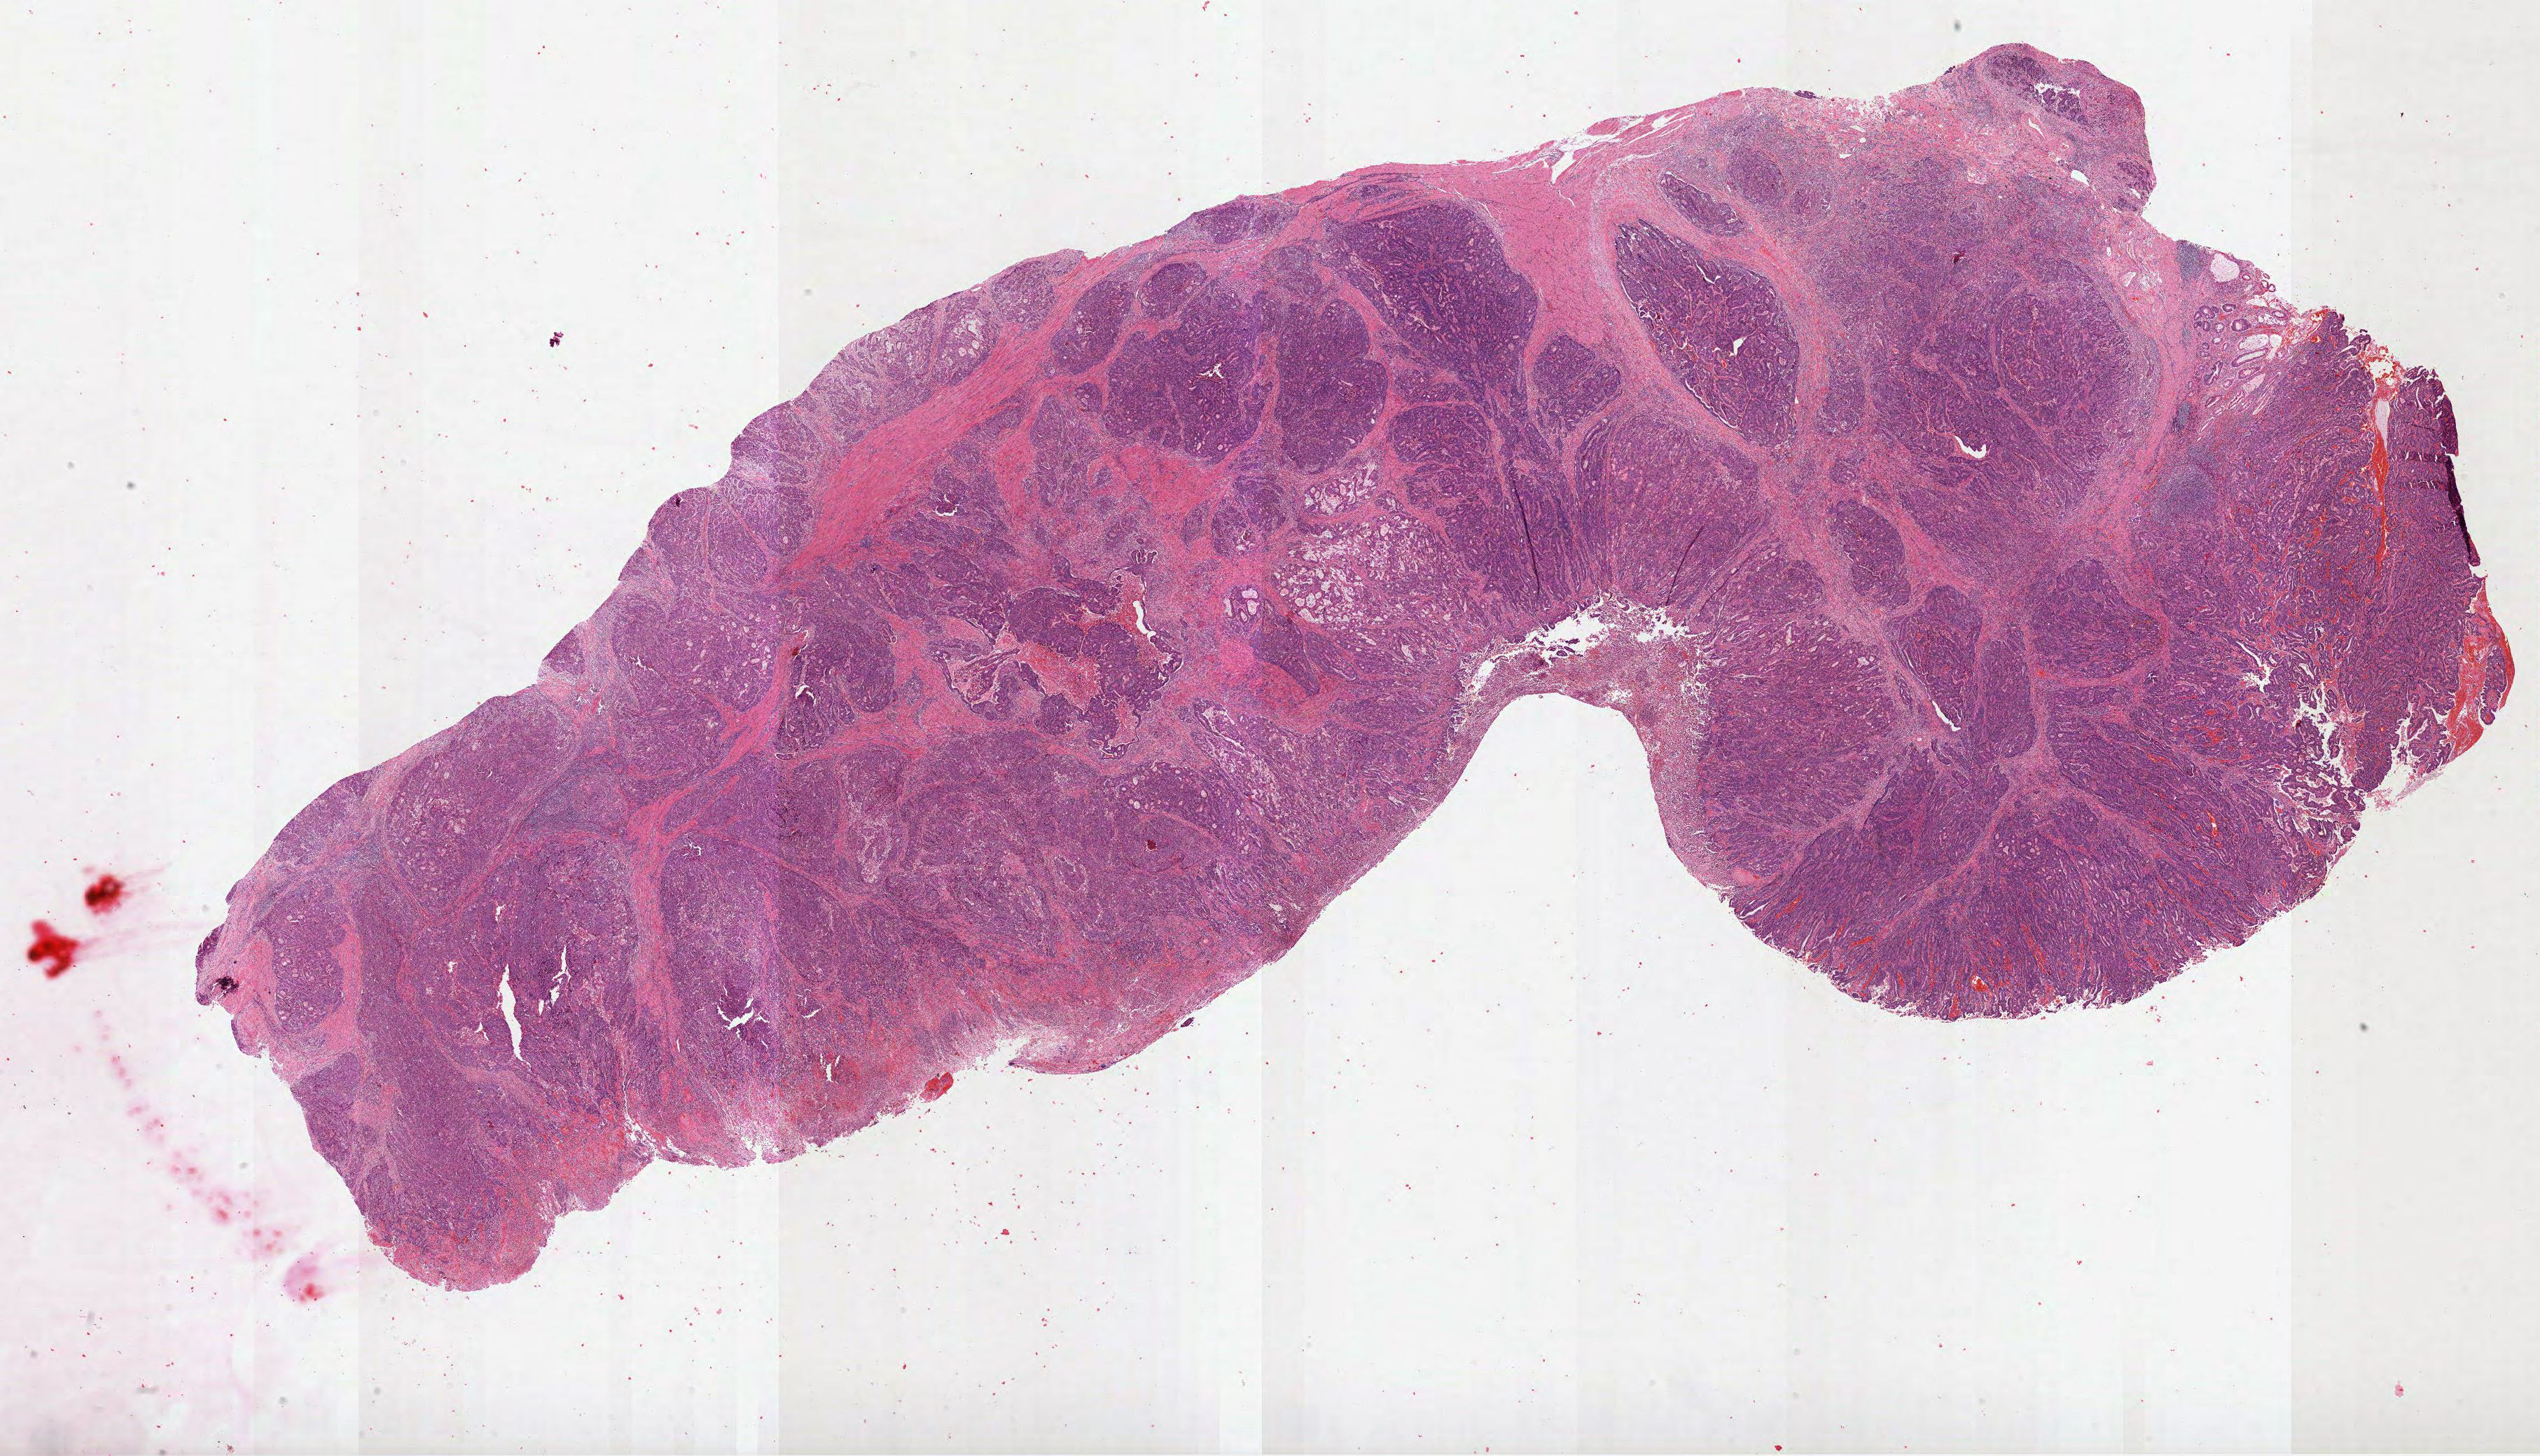
Digitized Hematoxylin and eosin (H&E) stained tissue section (whole slide), whole scanned area (about 29.2 x 16.8 mm, from a 40x scan) shown as a low-resolution overview. Formalin-fixed paraffin-embedded (FFPE) diagnostic section. Sample: primary tumour, stomach. Patient: male, age at initial diagnosis 63 years. Histologic grade: G3 (poorly differentiated).
• AJCC pathologic stage: IIIC
• lymph nodes positive (case pathology): 8 of 17 examined
• pathologic diagnosis: Adenocarcinoma, intestinal type